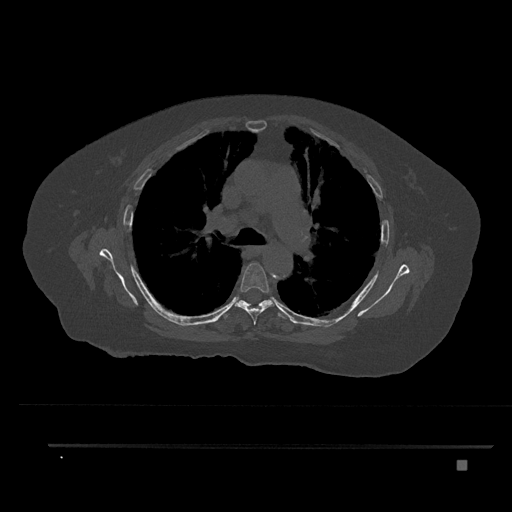
CT including the spine, one axial slice; position 556 of 797 along the scan axis; bone window (W 1800 / L 400 HU); 0.5 mm slice thickness; 512 × 512 image matrix, field of view 437 × 437 mm. Patient: female, 76 years. Case-level facts recorded for this patient, not image findings: primary cancer: lung; vertebrae with lytic lesions (as recorded): T11, L3.
Structures marked on this image (semi-automatic segmentation, software-assisted and operator-edited):
- T5 vertebra: box from (x=234, y=263) to (x=275, y=325) px
- T6 vertebra: (x=220, y=299)–(x=289, y=319)